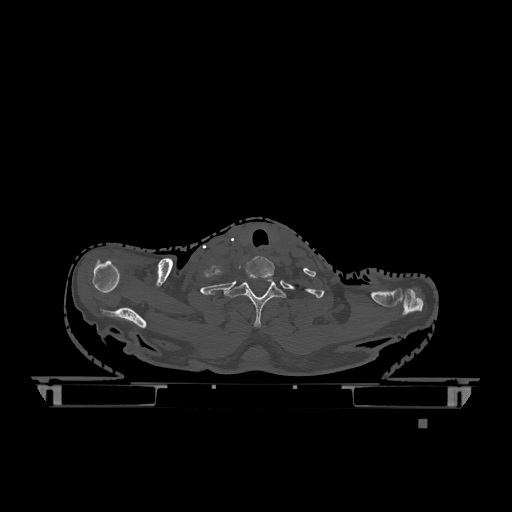
CT including the spine, one axial slice; slice 1005 of 1317 in the series (ordered by position); bone window (W 1800 / L 400 HU); 0.5 mm slice thickness; 512 × 512 image matrix, field of view 500 × 500 mm. Patient: female, 74 years. From the clinical record (not read from this slice): primary cancer: lung.
Structures marked on this image (semi-automatically segmented with operator editing):
- T1 vertebra: bounding box (x1, y1, x2, y2) in pixels: (224, 275, 286, 328)